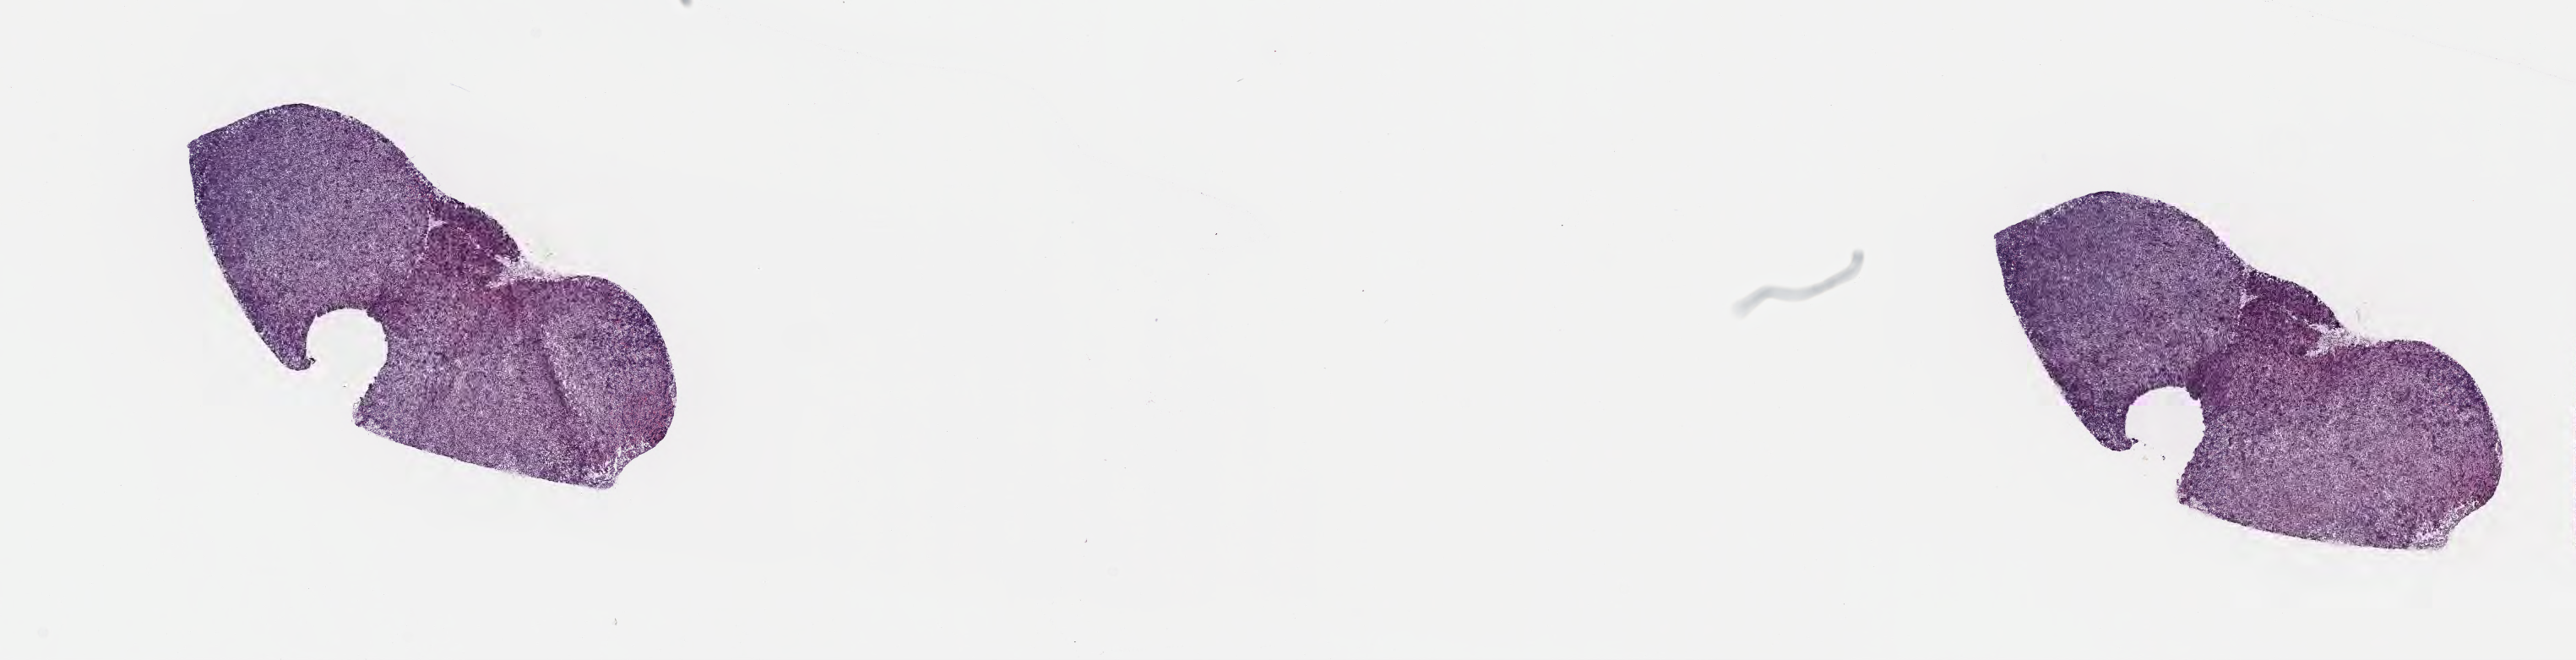
Whole-slide image, haematoxylin and eosin stain, low-resolution overview of the scanned area, about 24.7 x 6.3 mm. Frozen section (tissue freezing medium). Specimen: primary tumor. Site: mandible. Male, age 8 years at initial diagnosis. Slide review estimates, as recorded: tumor cells 90%, tumor nuclei 90%, stromal cells 0%, necrosis 10%, normal cells 0%. Infiltration values recorded for this section: lymphocyte infiltration 20%, monocyte infiltration 50%, neutrophil infiltration 20%.
• Ann Arbor stage (patient): Stage III
• histologic diagnosis: Burkitt lymphoma, NOS
• section: bottom of the tissue portion